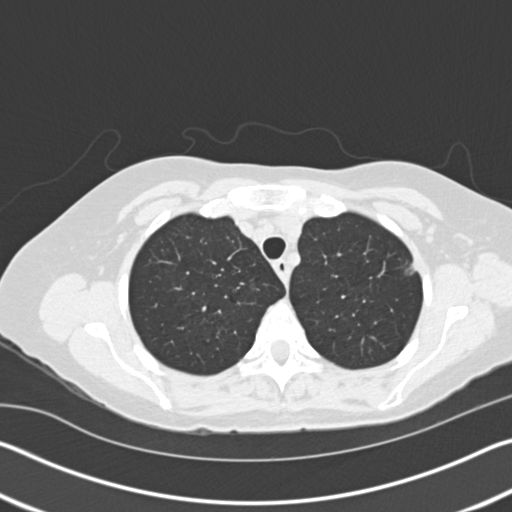
Low-dose screening chest CT, axial slice, first (baseline) screen, lung window (W 1500 / L -600 HU), standard (soft-tissue) reconstruction kernel (B30f), 120 kVp. Female, age 60 years at enrolment.
Expert reader's lesion annotation, box from (x=381, y=243) to (x=434, y=285) px. The screening reader recorded 2 non-calcified nodules or masses ≥4 mm on this exam; which of them this box marks is not recorded. Official screen result: positive, change unspecified: nodule(s) >= 4 mm or enlarging nodule(s), mass(es), or other non-specific abnormalities suspicious for lung cancer.